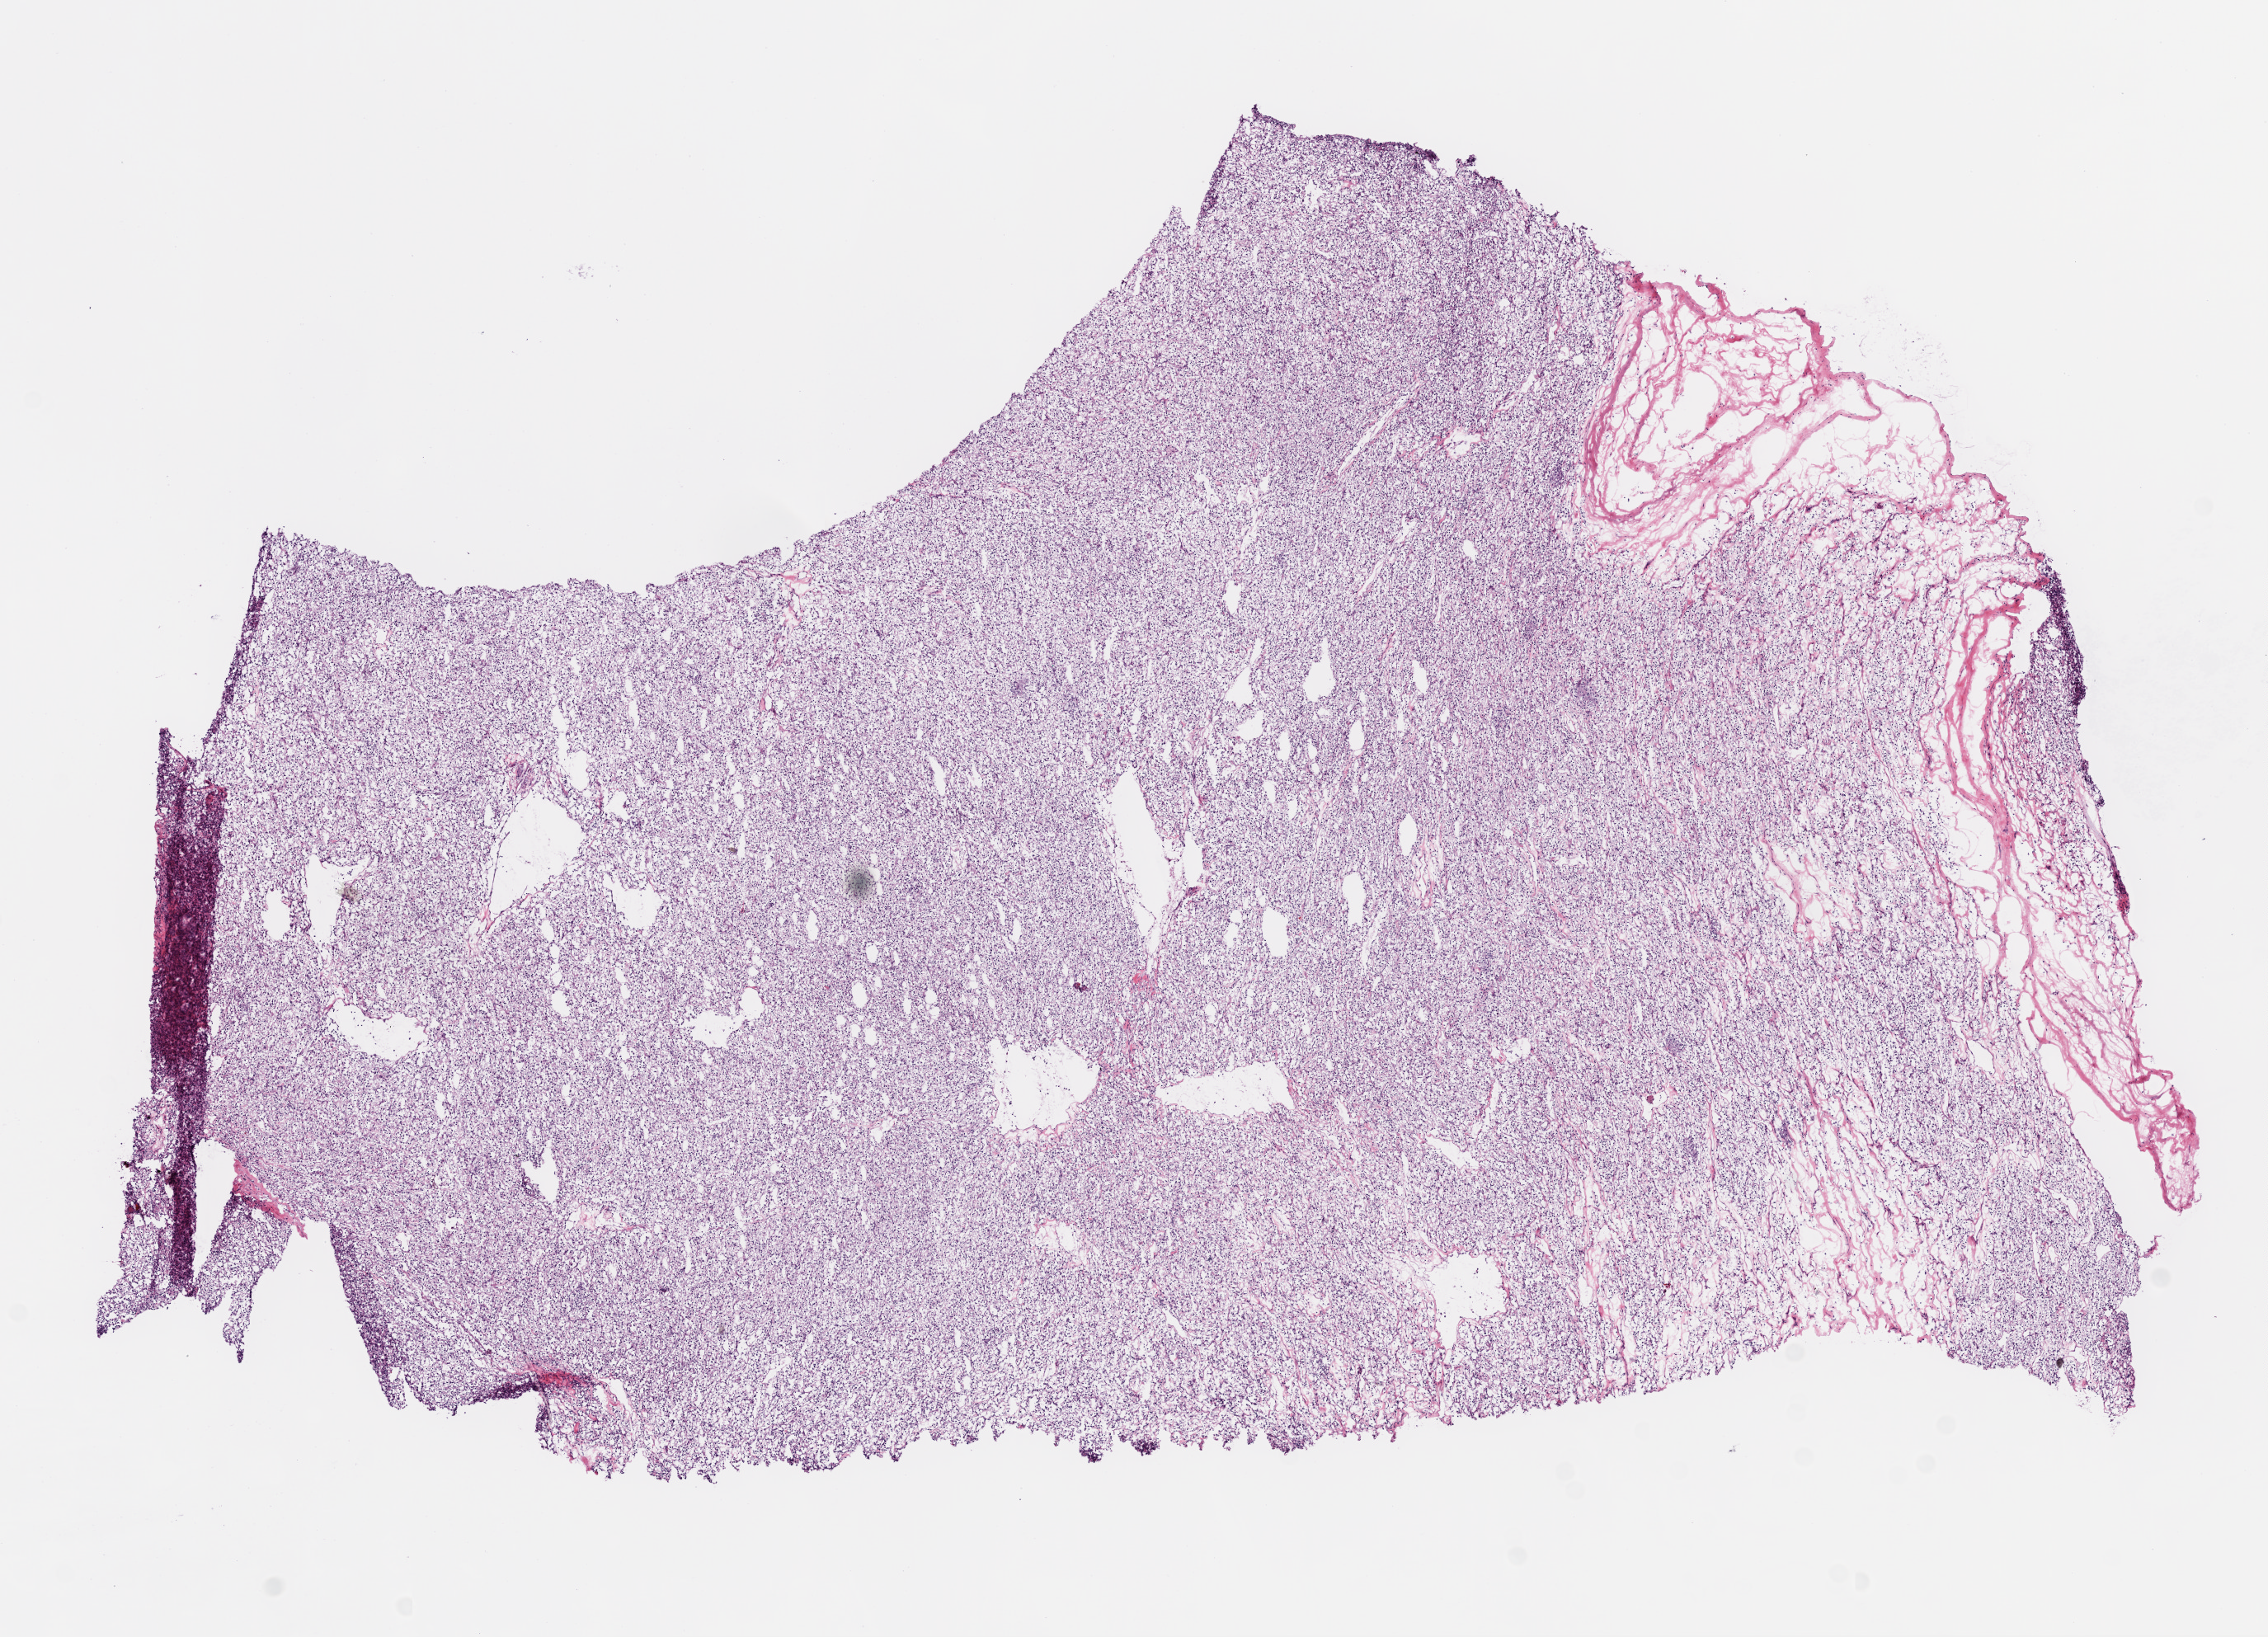
Digitized H&E-stained tissue section (whole slide), a low-resolution overview of the entire scanned area, about 11.0 x 8.0 mm. Frozen section from the bottom of the tissue portion. Sample: primary tumour, kidney. Male patient; age at initial diagnosis 79 years. Histologic grade: G3 (poorly differentiated). Slide review estimates, as recorded: tumour cells 90%, tumour nuclei 80%, normal cells 0%, stromal cells 10%, necrosis 0%. Infiltration values recorded for this section: lymphocyte infiltration 15%, monocyte infiltration 0%, neutrophil infiltration 0%.
* AJCC pathologic stage: II
* histologic diagnosis: Clear cell adenocarcinoma, NOS
* lymph nodes positive (case pathology): 0 of 1 examined